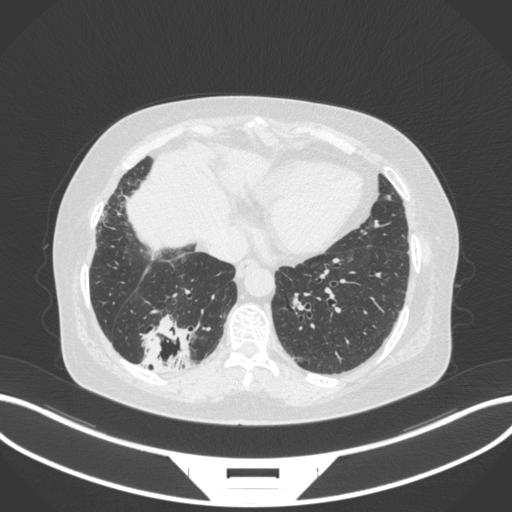
Chest CT, one axial slice. Reconstruction kernel B31f. 120 kVp. Lung window (W 1500 / L -600 HU). 1 mm slice thickness. 512 × 512 image matrix, field of view 400 × 400 mm. Patient: female, 65 years. From the clinical record (not read from this slice): clinical TNM (as recorded): T2b N1 M0; histopathological grade: G1.
Outlined on this slice (rectangle marked by the reading radiologist):
- lung tumour (recorded histology: adenocarcinoma): bounding box [x1, y1, x2, y2] px = [135, 312, 194, 371]